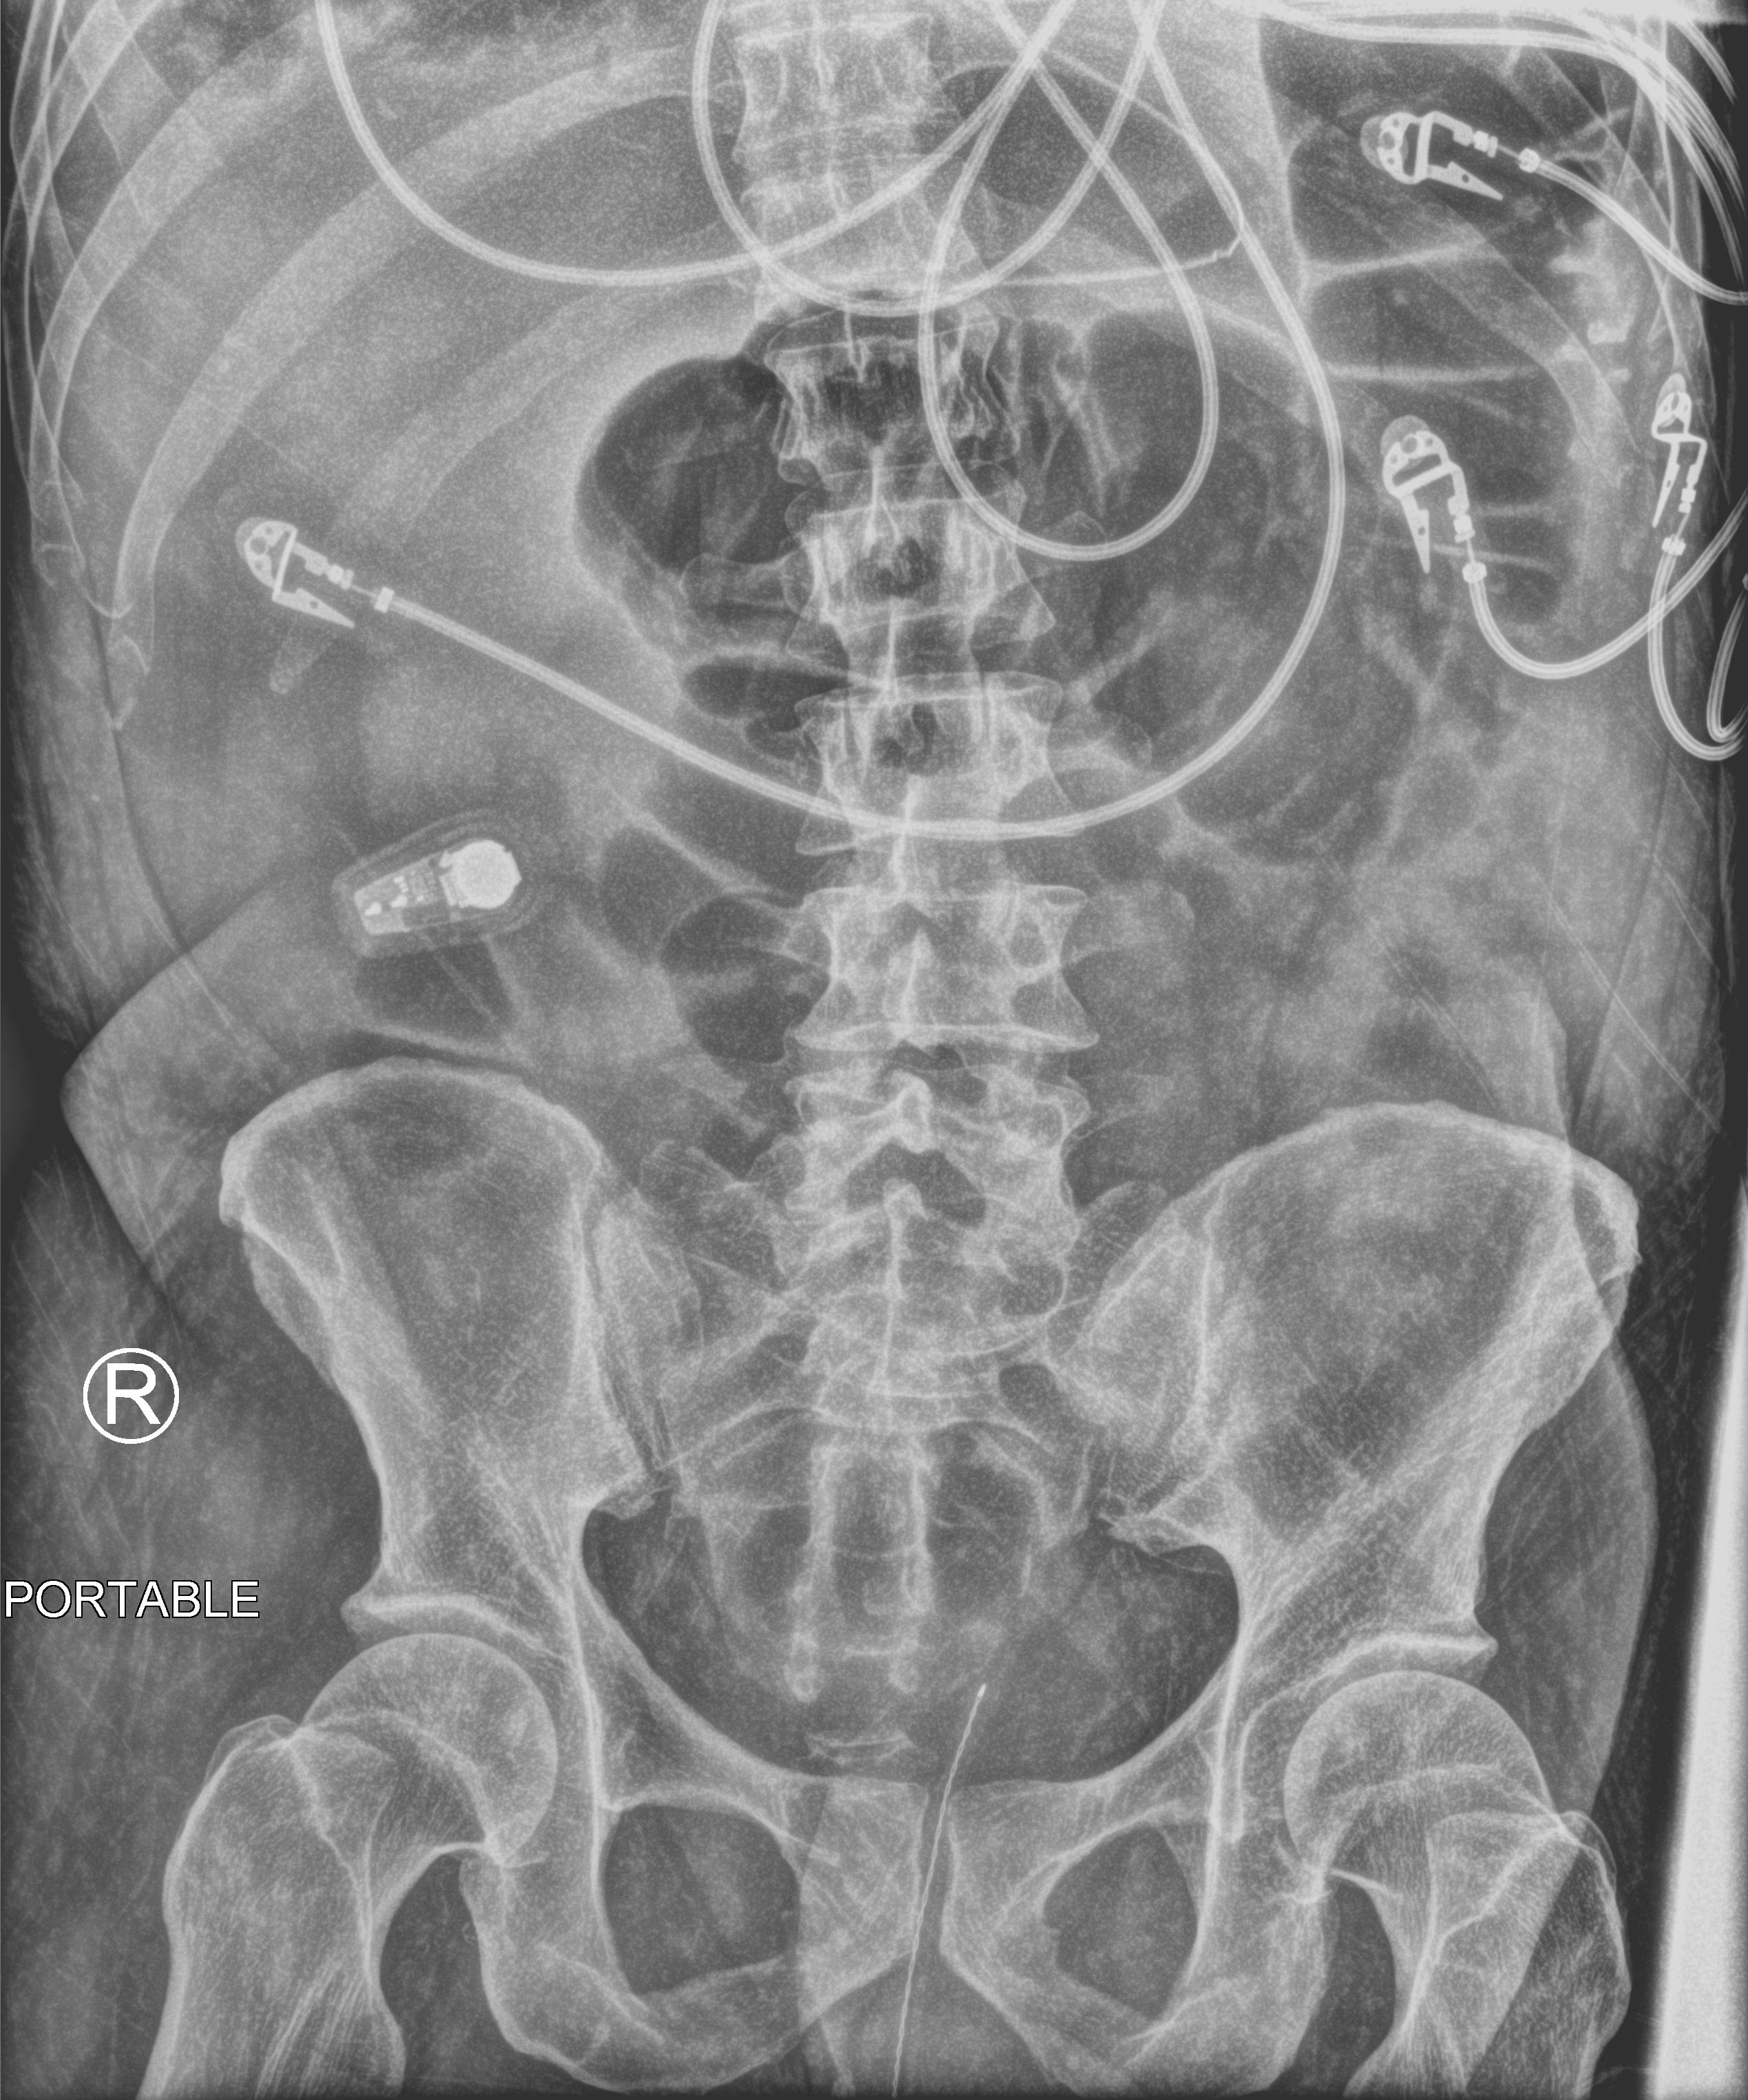
Bedside abdomen radiograph (computed radiography), anteroposterior (AP) projection. Patient hospitalised with COVID-19; male, aged 18–59 years.
From the hospital-stay record, not from the radiograph (when in the stay this image was taken is not recorded): mechanically ventilated during this hospital stay: yes; admitted to intensive care during this hospital stay: yes.